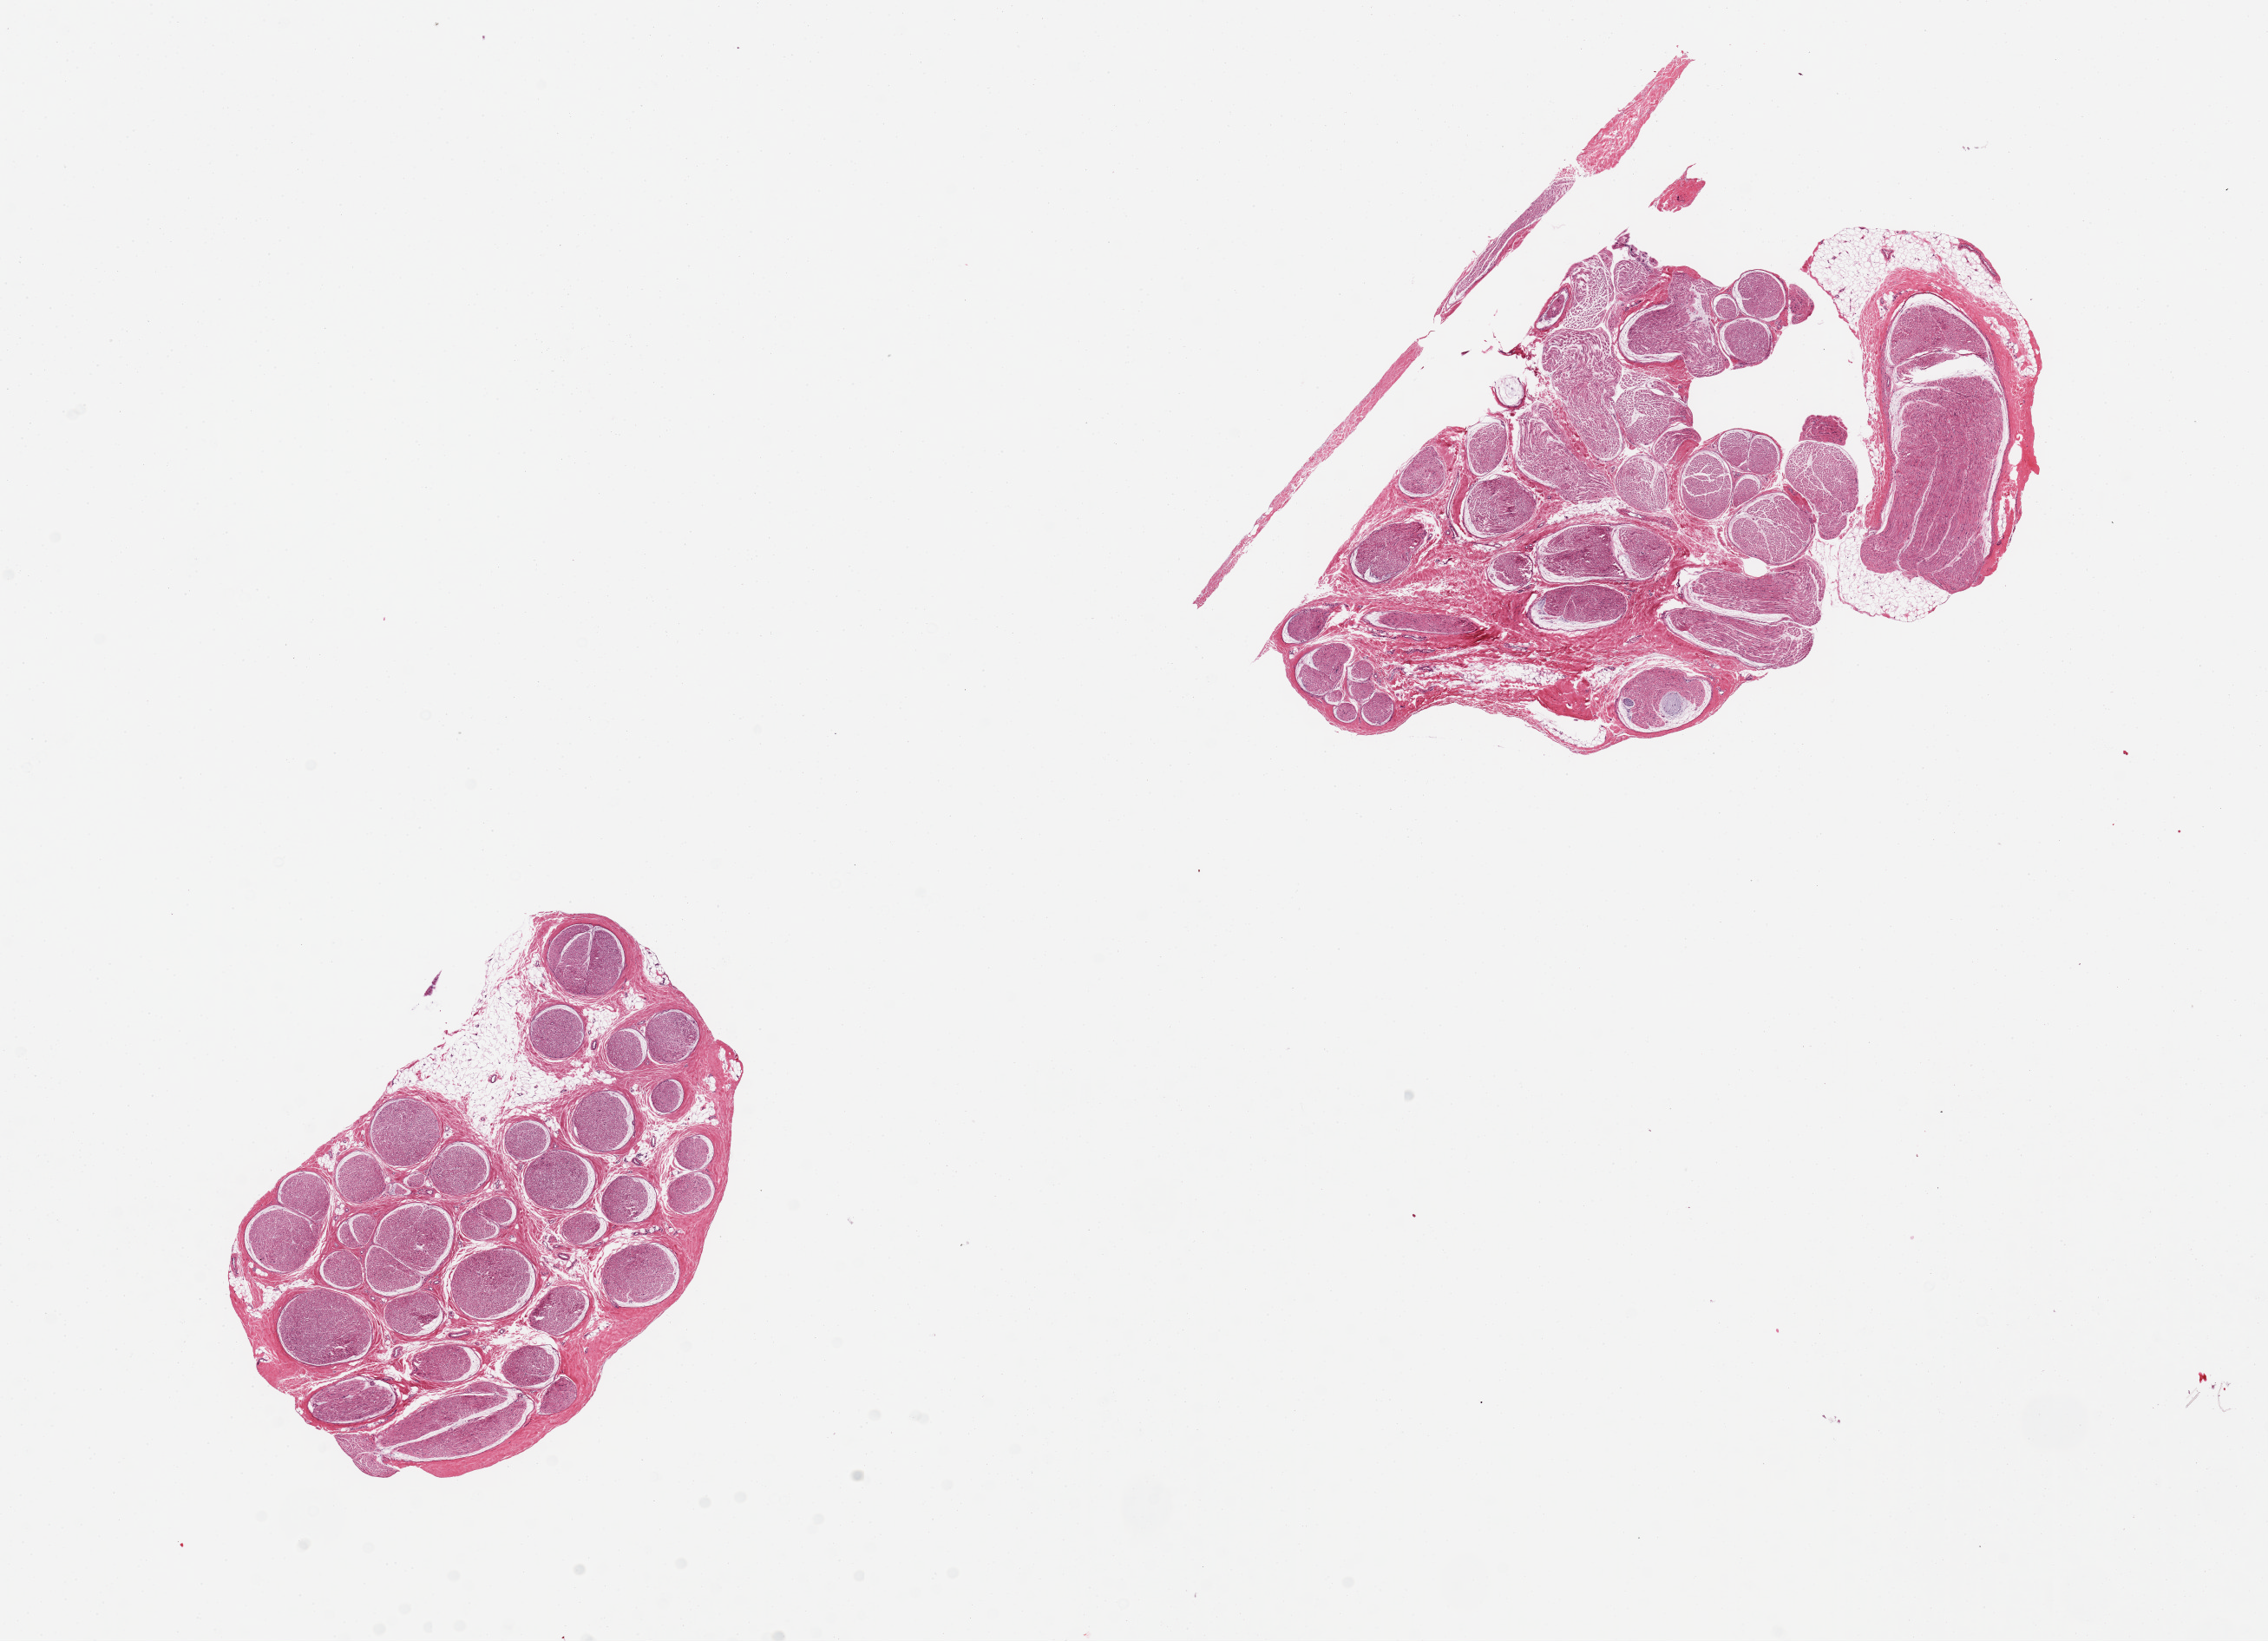
Hematoxylin and eosin (H&E) whole-slide image, whole scanned area (about 20.7 x 15.0 mm, acquisition: 20x scan) shown as a low-resolution overview. PAXgene-fixed, paraffin-embedded tissue. Section of tibial nerve (target tissue). Tissue donor sample. Donor: male.
* pathologist's review note for this sample: 2 pieces